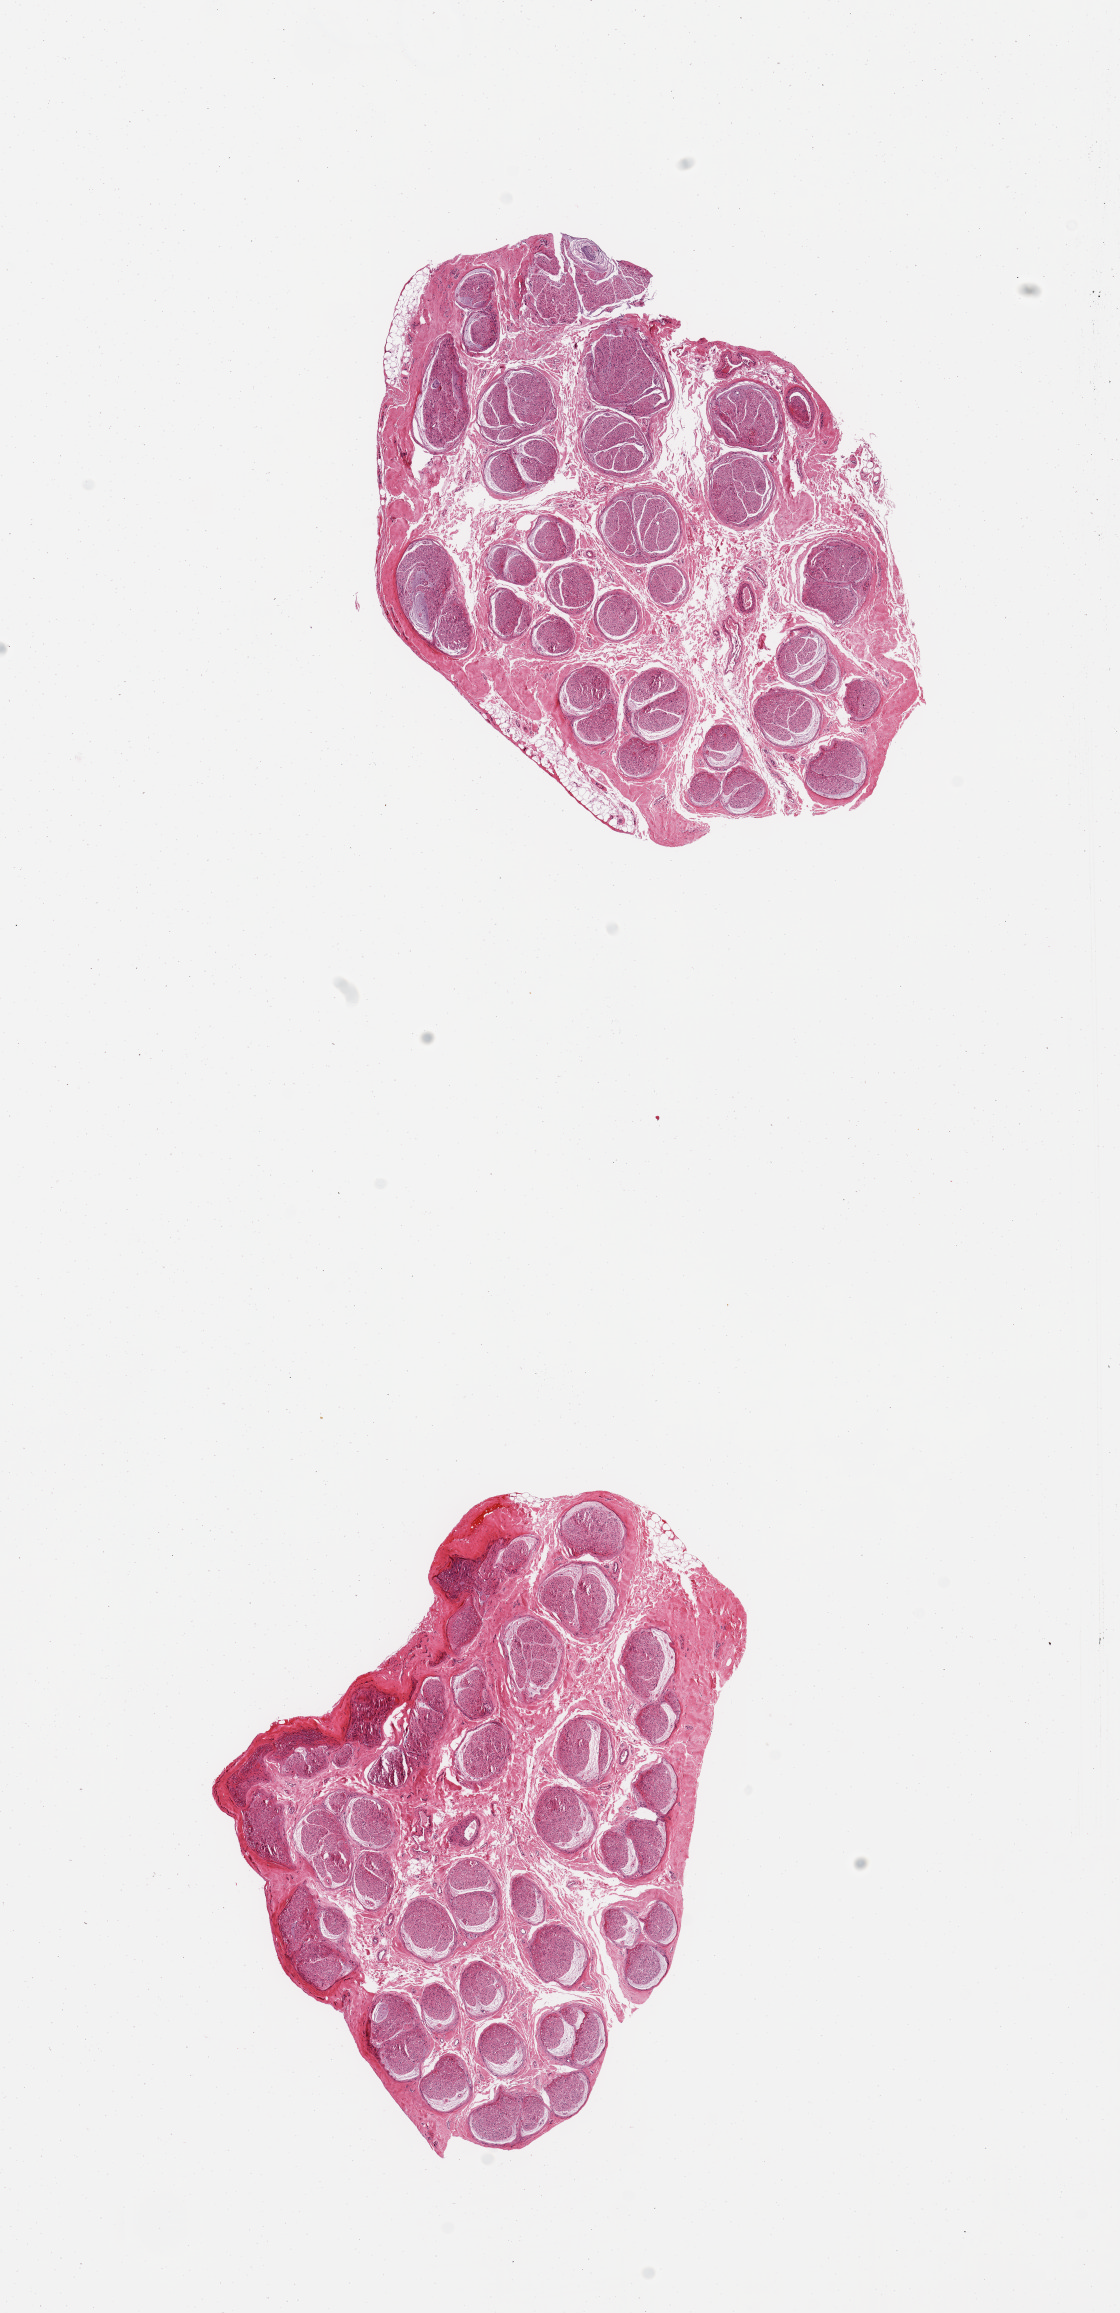
Digitized haematoxylin and eosin-stained section, a low-resolution overview of the entire scanned area, about 8.9 x 18.3 mm; PAXgene-fixed paraffin-embedded (PFPE) section; sampled site (target tissue): tibial nerve; tissue donor sample. Male donor.
Reviewer comment on this tissue sample: 2 pieces; nerve contains hyalinized small blood vessels; well trimmed; minimal fat.